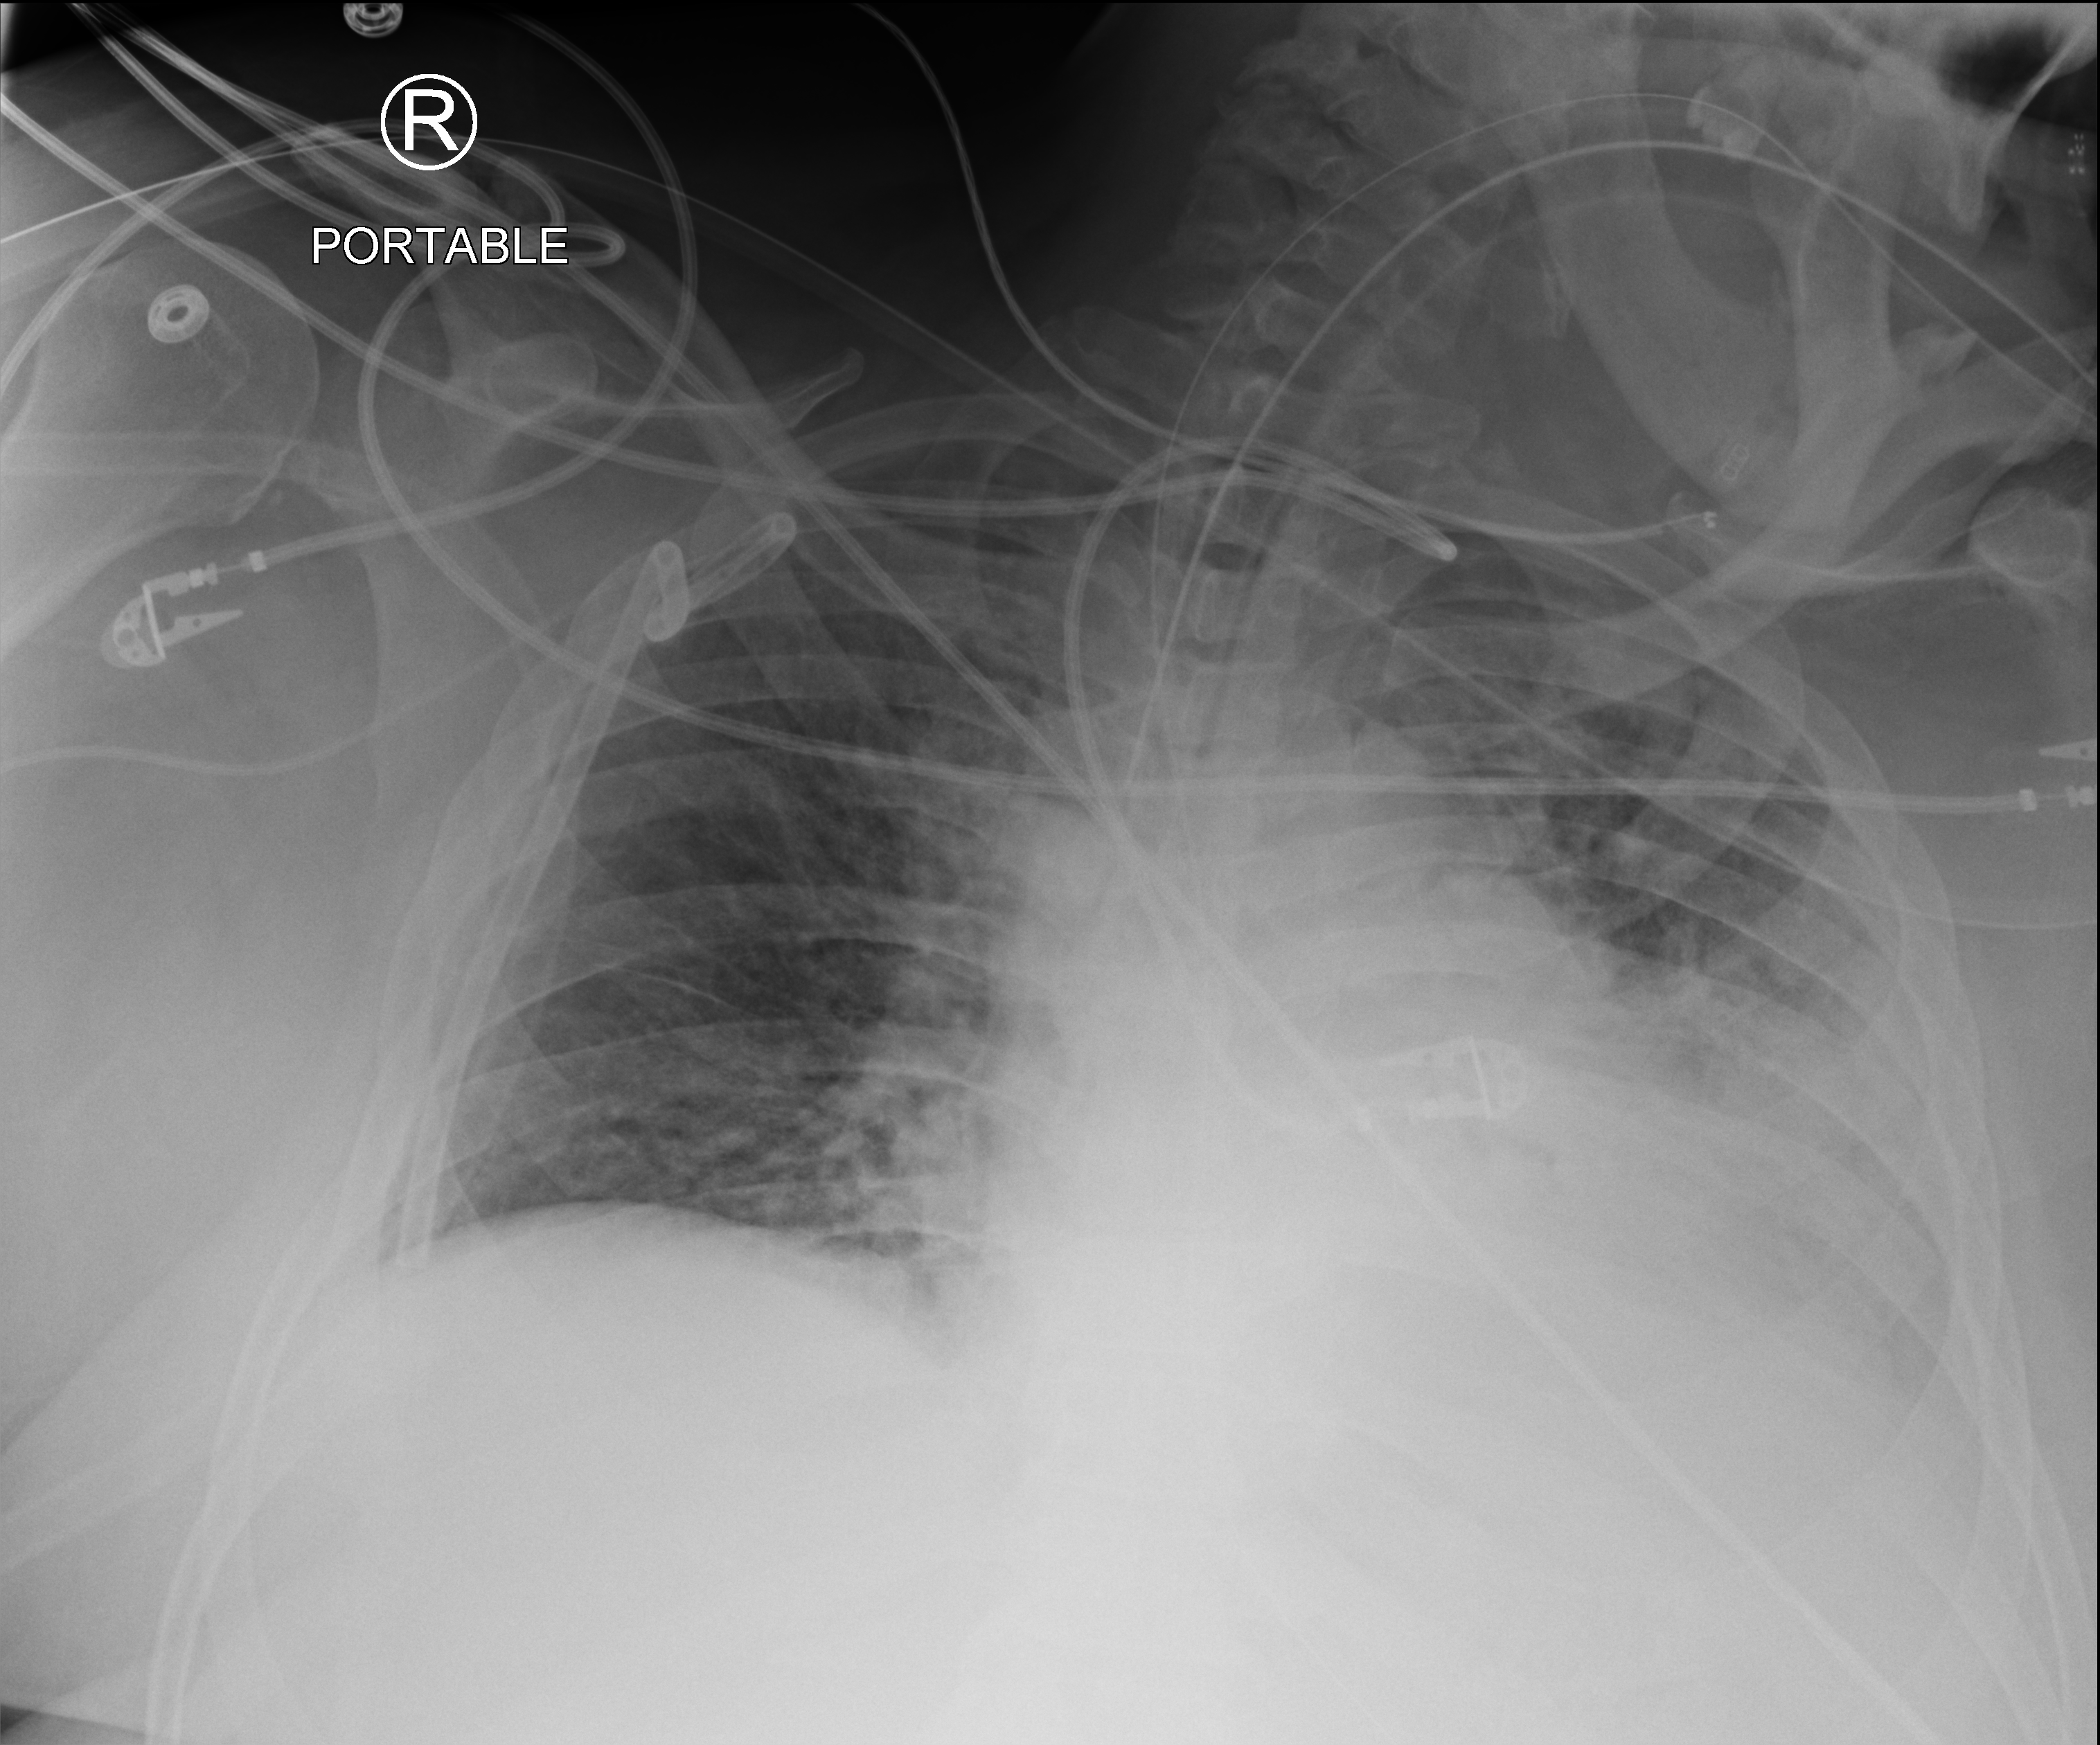
Chest X-ray (portable); anteroposterior (AP) projection. Patient hospitalised with COVID-19; male, aged 60–74 years.
From the hospital-stay record, not from the radiograph (when in the stay this image was taken is not recorded): admitted to intensive care during this hospital stay: yes.